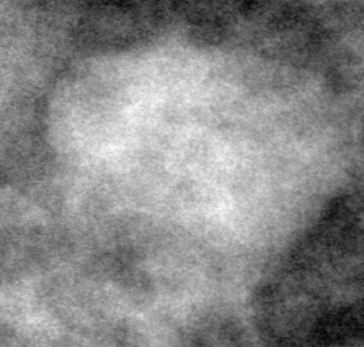
Cropped region of a digitized screen-film mammogram centred on a radiologist-marked abnormality; right breast; CC view; BI-RADS breast density category 2 (scale 1–4).
Finding: mass, shape oval, margins microlobulated; BI-RADS assessment category 0 (incomplete: needs additional imaging); pathology result (as recorded, not read from the image): benign.